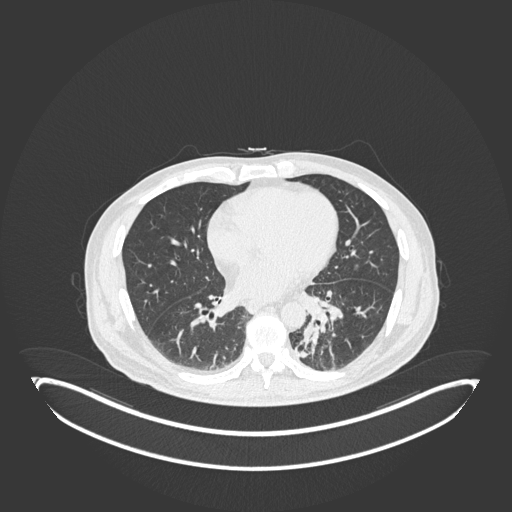
Chest CT, one axial slice. Reconstruction kernel B30f. Lung window (W 1500 / L -600 HU). 512 × 512 image matrix, field of view 500 × 500 mm. Male patient, age 72 years. From the clinical record (not read from this slice): clinical TNM (as recorded): T2b N0 M1.
Structures marked on this image (rectangle marked by the reading radiologist):
- lung tumour (recorded histology: adenocarcinoma): bounding box <295,318,319,360> (left, top, right, bottom; pixels)